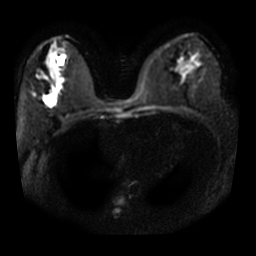
Breast MRI, one axial slice; slice 18 of 32 in the series (ordered by position); diffusion-weighted series; image 2 of 4 stored at this slice position (different b-values; order by instance number); 3 T; 256 × 256 image matrix. Female patient.
Structures marked on this image (expert manual segmentation):
- tumour on diffusion-weighted imaging: bounding box (x1, y1, x2, y2) in pixels: (44, 96, 56, 106)